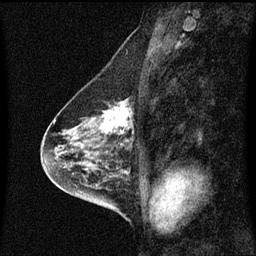
Breast MRI (dynamic contrast-enhanced), one sagittal slice. Slice 30 of 60 in the series (ordered by position). Dynamic contrast-enhanced series, image 2 of 3 at this slice position (ordered by acquisition). 1.5 T. TE 4.2 ms, TR 8.4 ms. 256 × 256 image matrix. Female patient, age 58 years.
Structures marked on this image (semi-automatic segmentation, software-assisted and operator-edited):
- analysis volume of interest (the breast-tissue region the enhancement analysis was run in; not a lesion): bounding box <86,98,134,143> (left, top, right, bottom; pixels)
- tumour enhancement mask (voxels above the 70 % enhancement threshold inside the analysis volume of interest): <90,102,134,135>